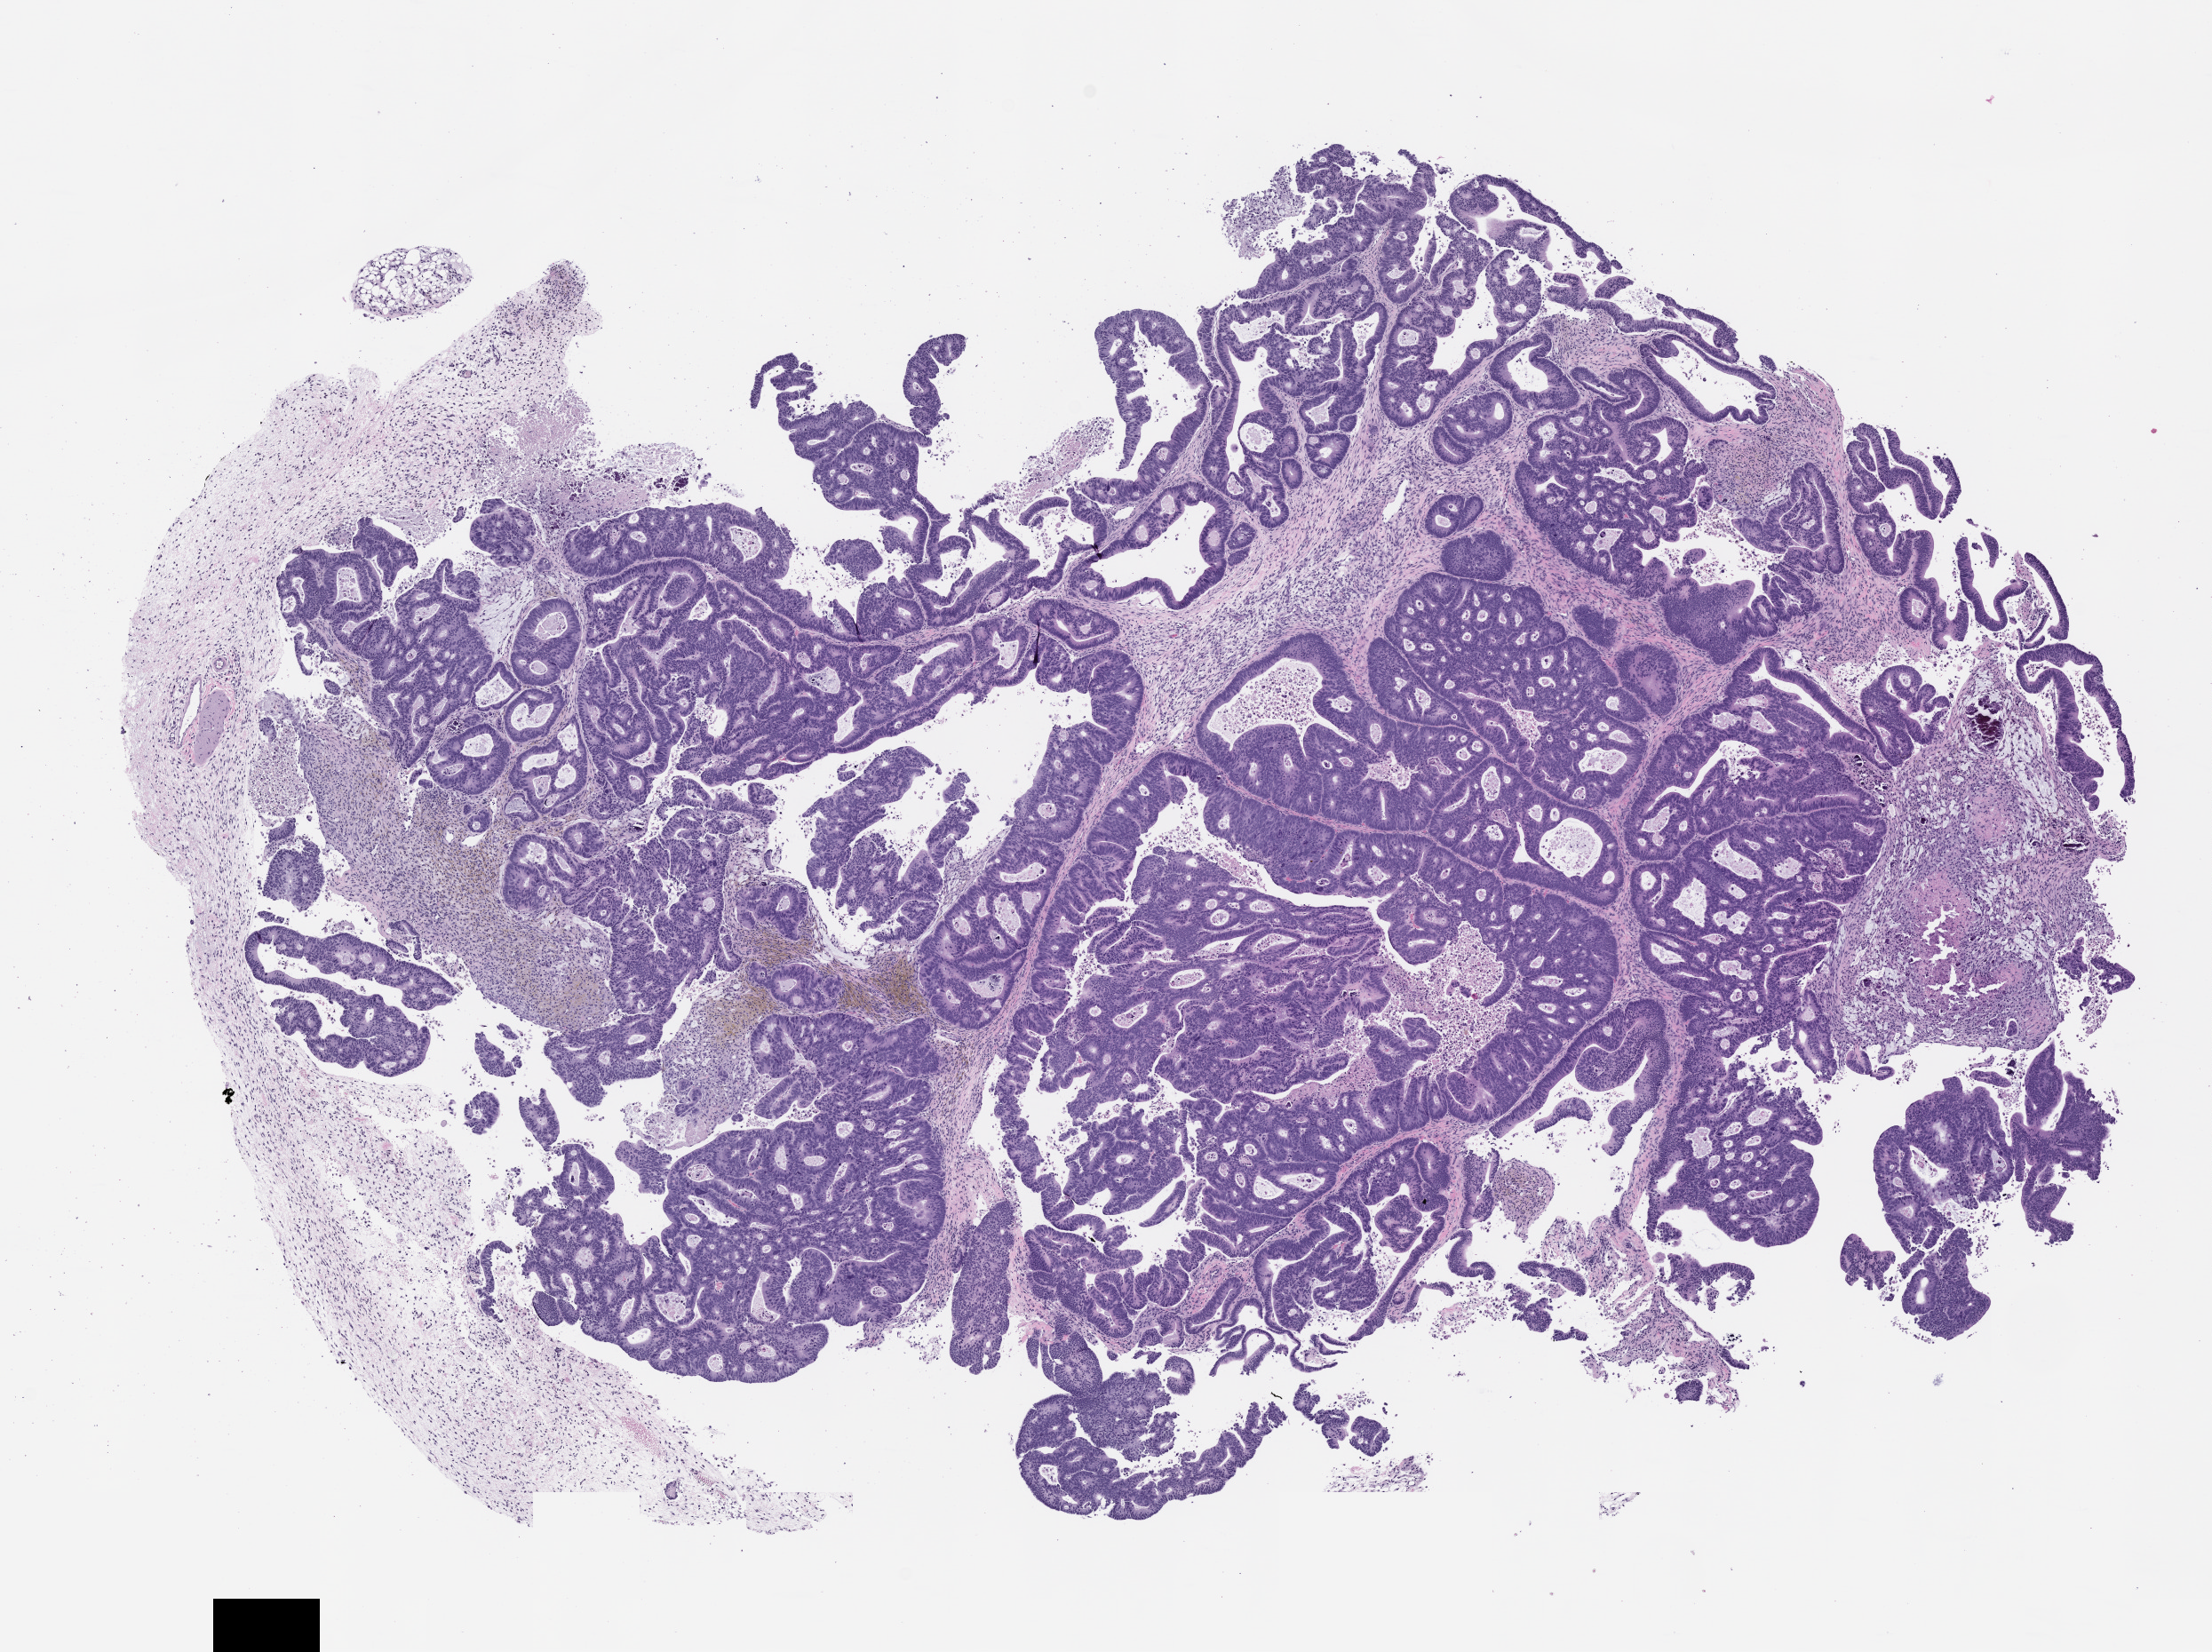
Haematoxylin and eosin whole-slide image of a patient-derived xenograft (PDX) tumor grown in a mouse, passage 0 — low-resolution overview of the scanned area, about 10.0 x 7.5 mm. Formalin-fixed paraffin-embedded section. Tumor site category: colon.
- originating patient diagnosis: Colon Adenocarcinoma